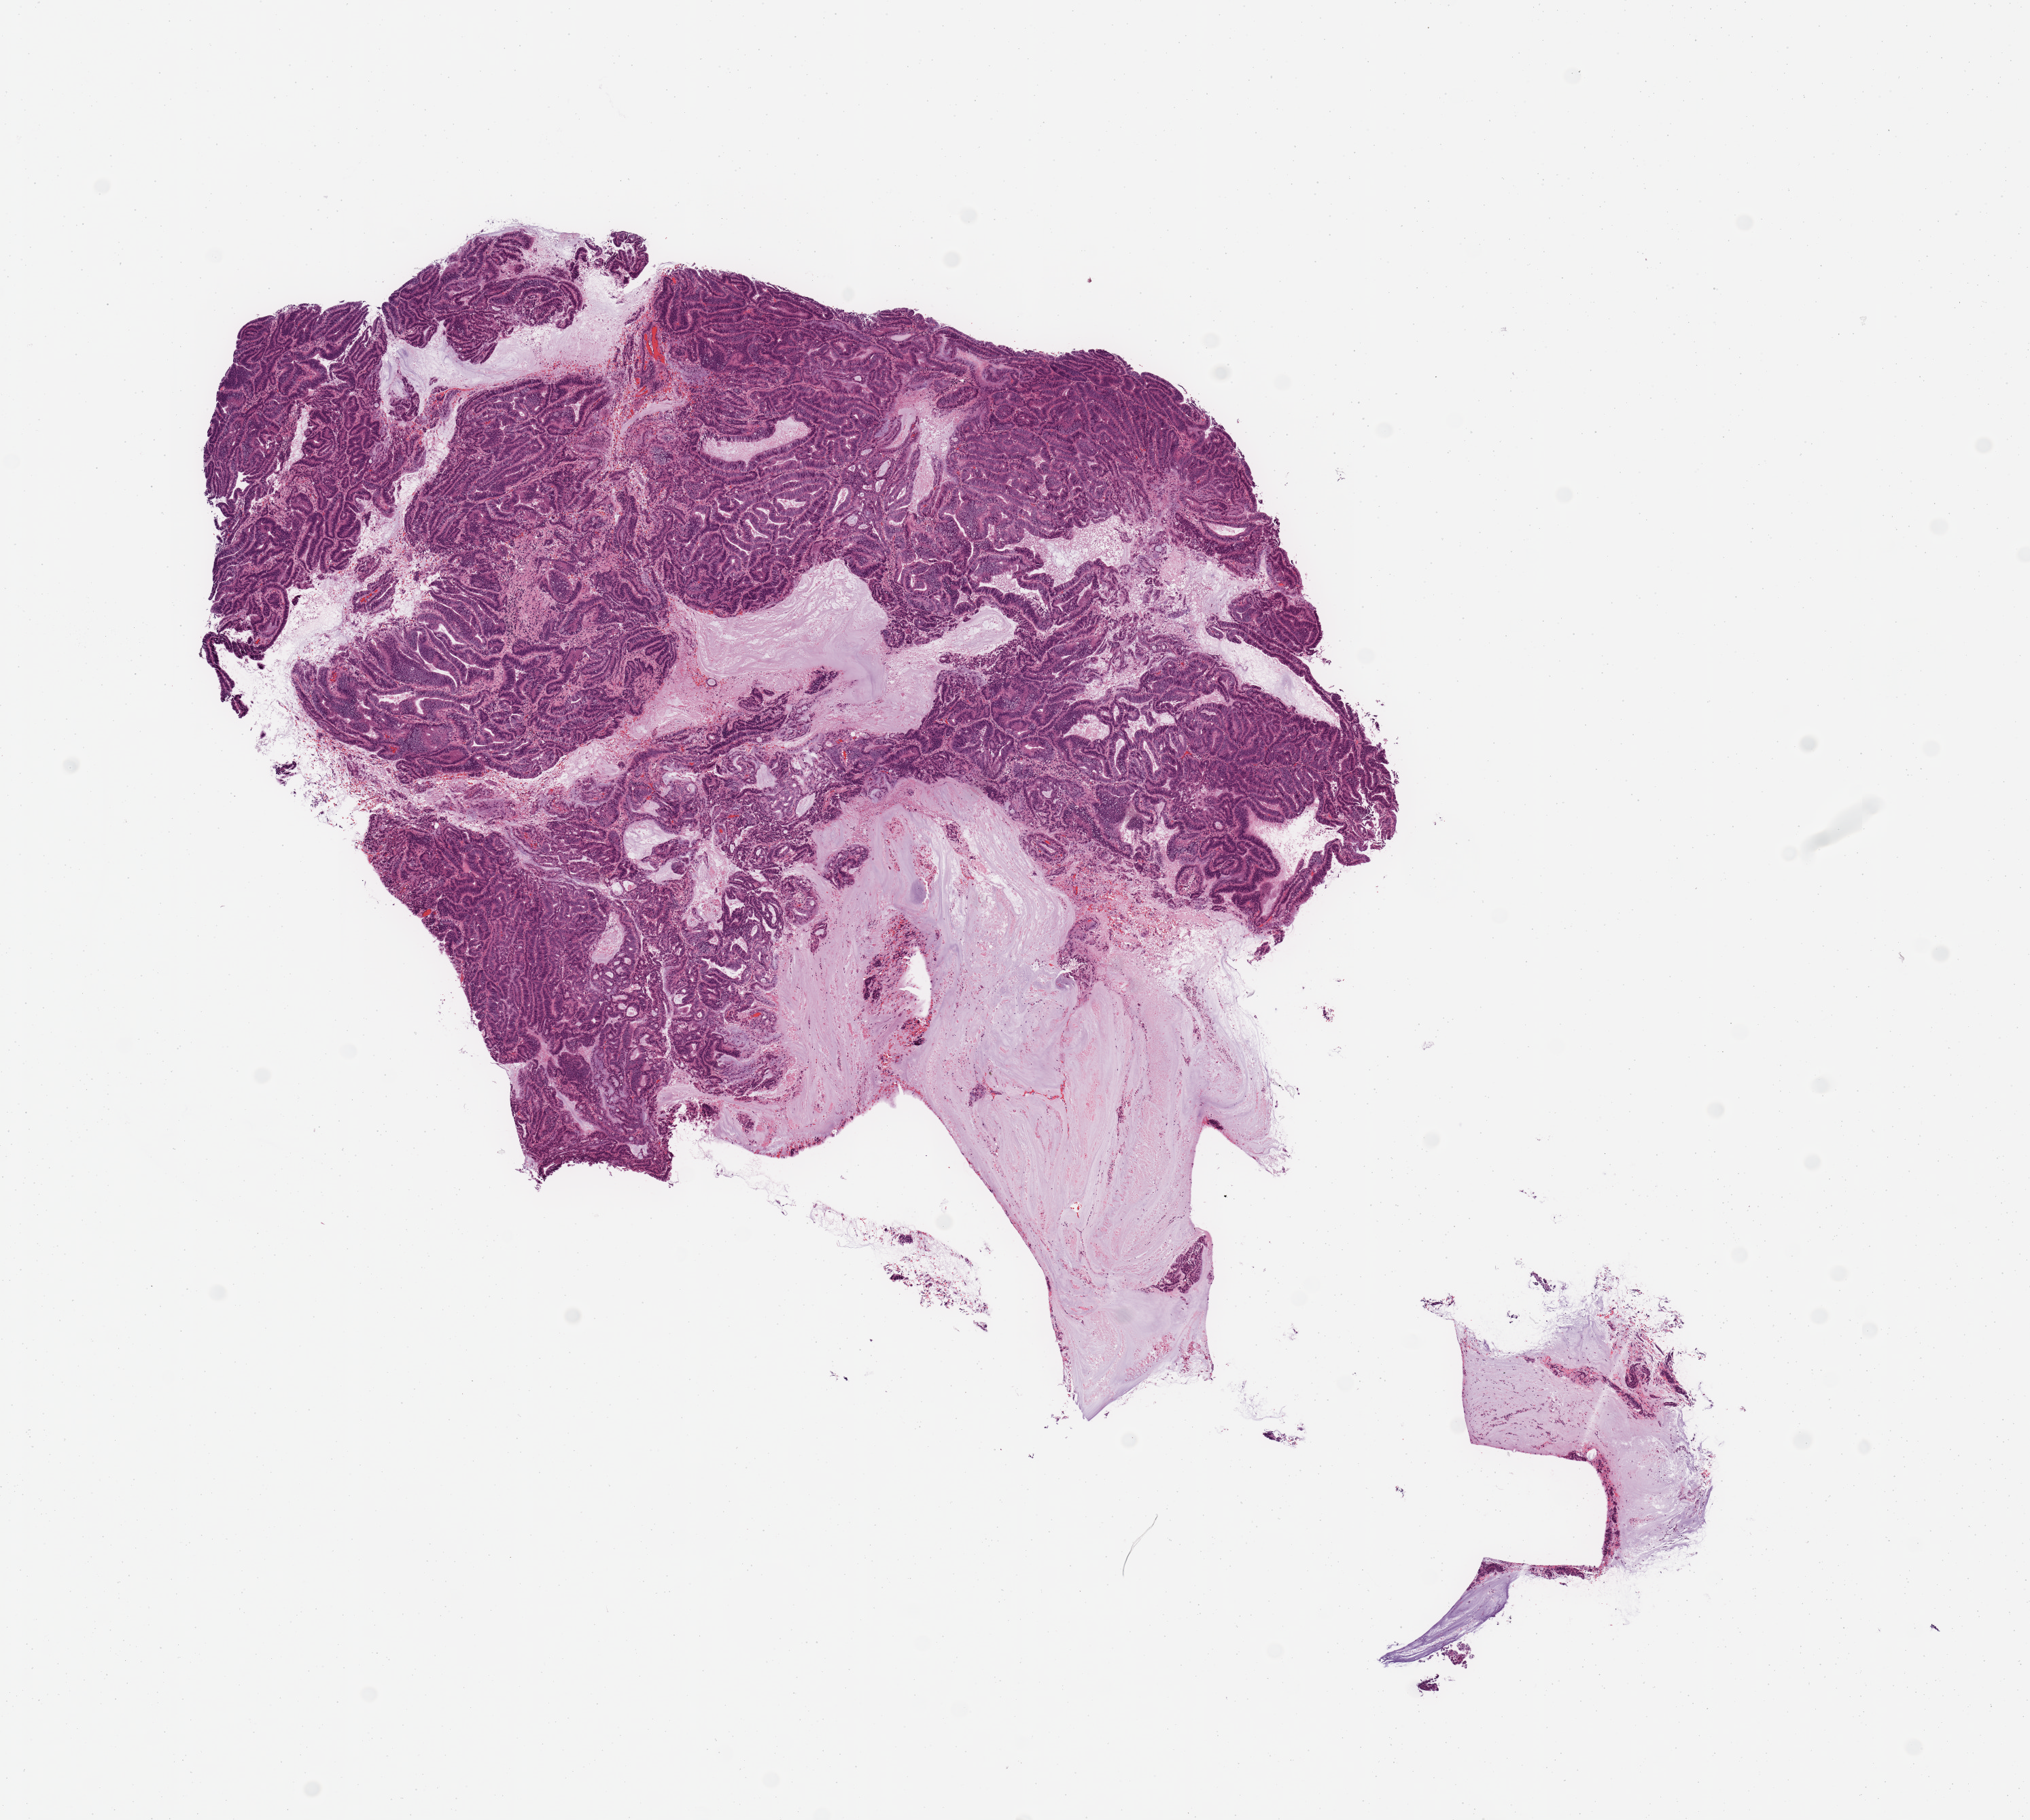
Hematoxylin and eosin (H&E) stained whole-slide image — shown as a low-resolution overview of the whole scanned area (about 11.8 x 10.6 mm, slide scanned at 20x), tumour tissue sample, sampled site: uterus. Female, 64 y/o. Histologic grade: G1 (well differentiated). Composition of this section per pathologist review: tumour nuclei 90%, necrosis 5%.
- diagnosis: Endometrioid adenocarcinoma, NOS
- AJCC pathologic stage: I
- primary tumour site (as recorded): anterior endometrium